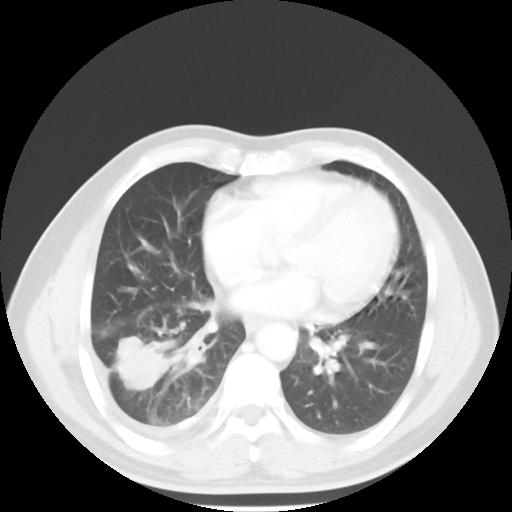
Chest CT, one axial slice. Position 22 of 56 along the scan axis. 120 kVp. Lung window (W 1500 / L -600 HU). 5 mm slice thickness. 512 × 512 image matrix. Patient: male, 56 years. Case-level facts recorded for this patient, not image findings: clinical TNM (as recorded): T2 N3 M1.
Outlined on this slice (bounding box drawn by a radiologist):
- lung tumour (recorded histology: adenocarcinoma): box from (x=116, y=333) to (x=178, y=390) px